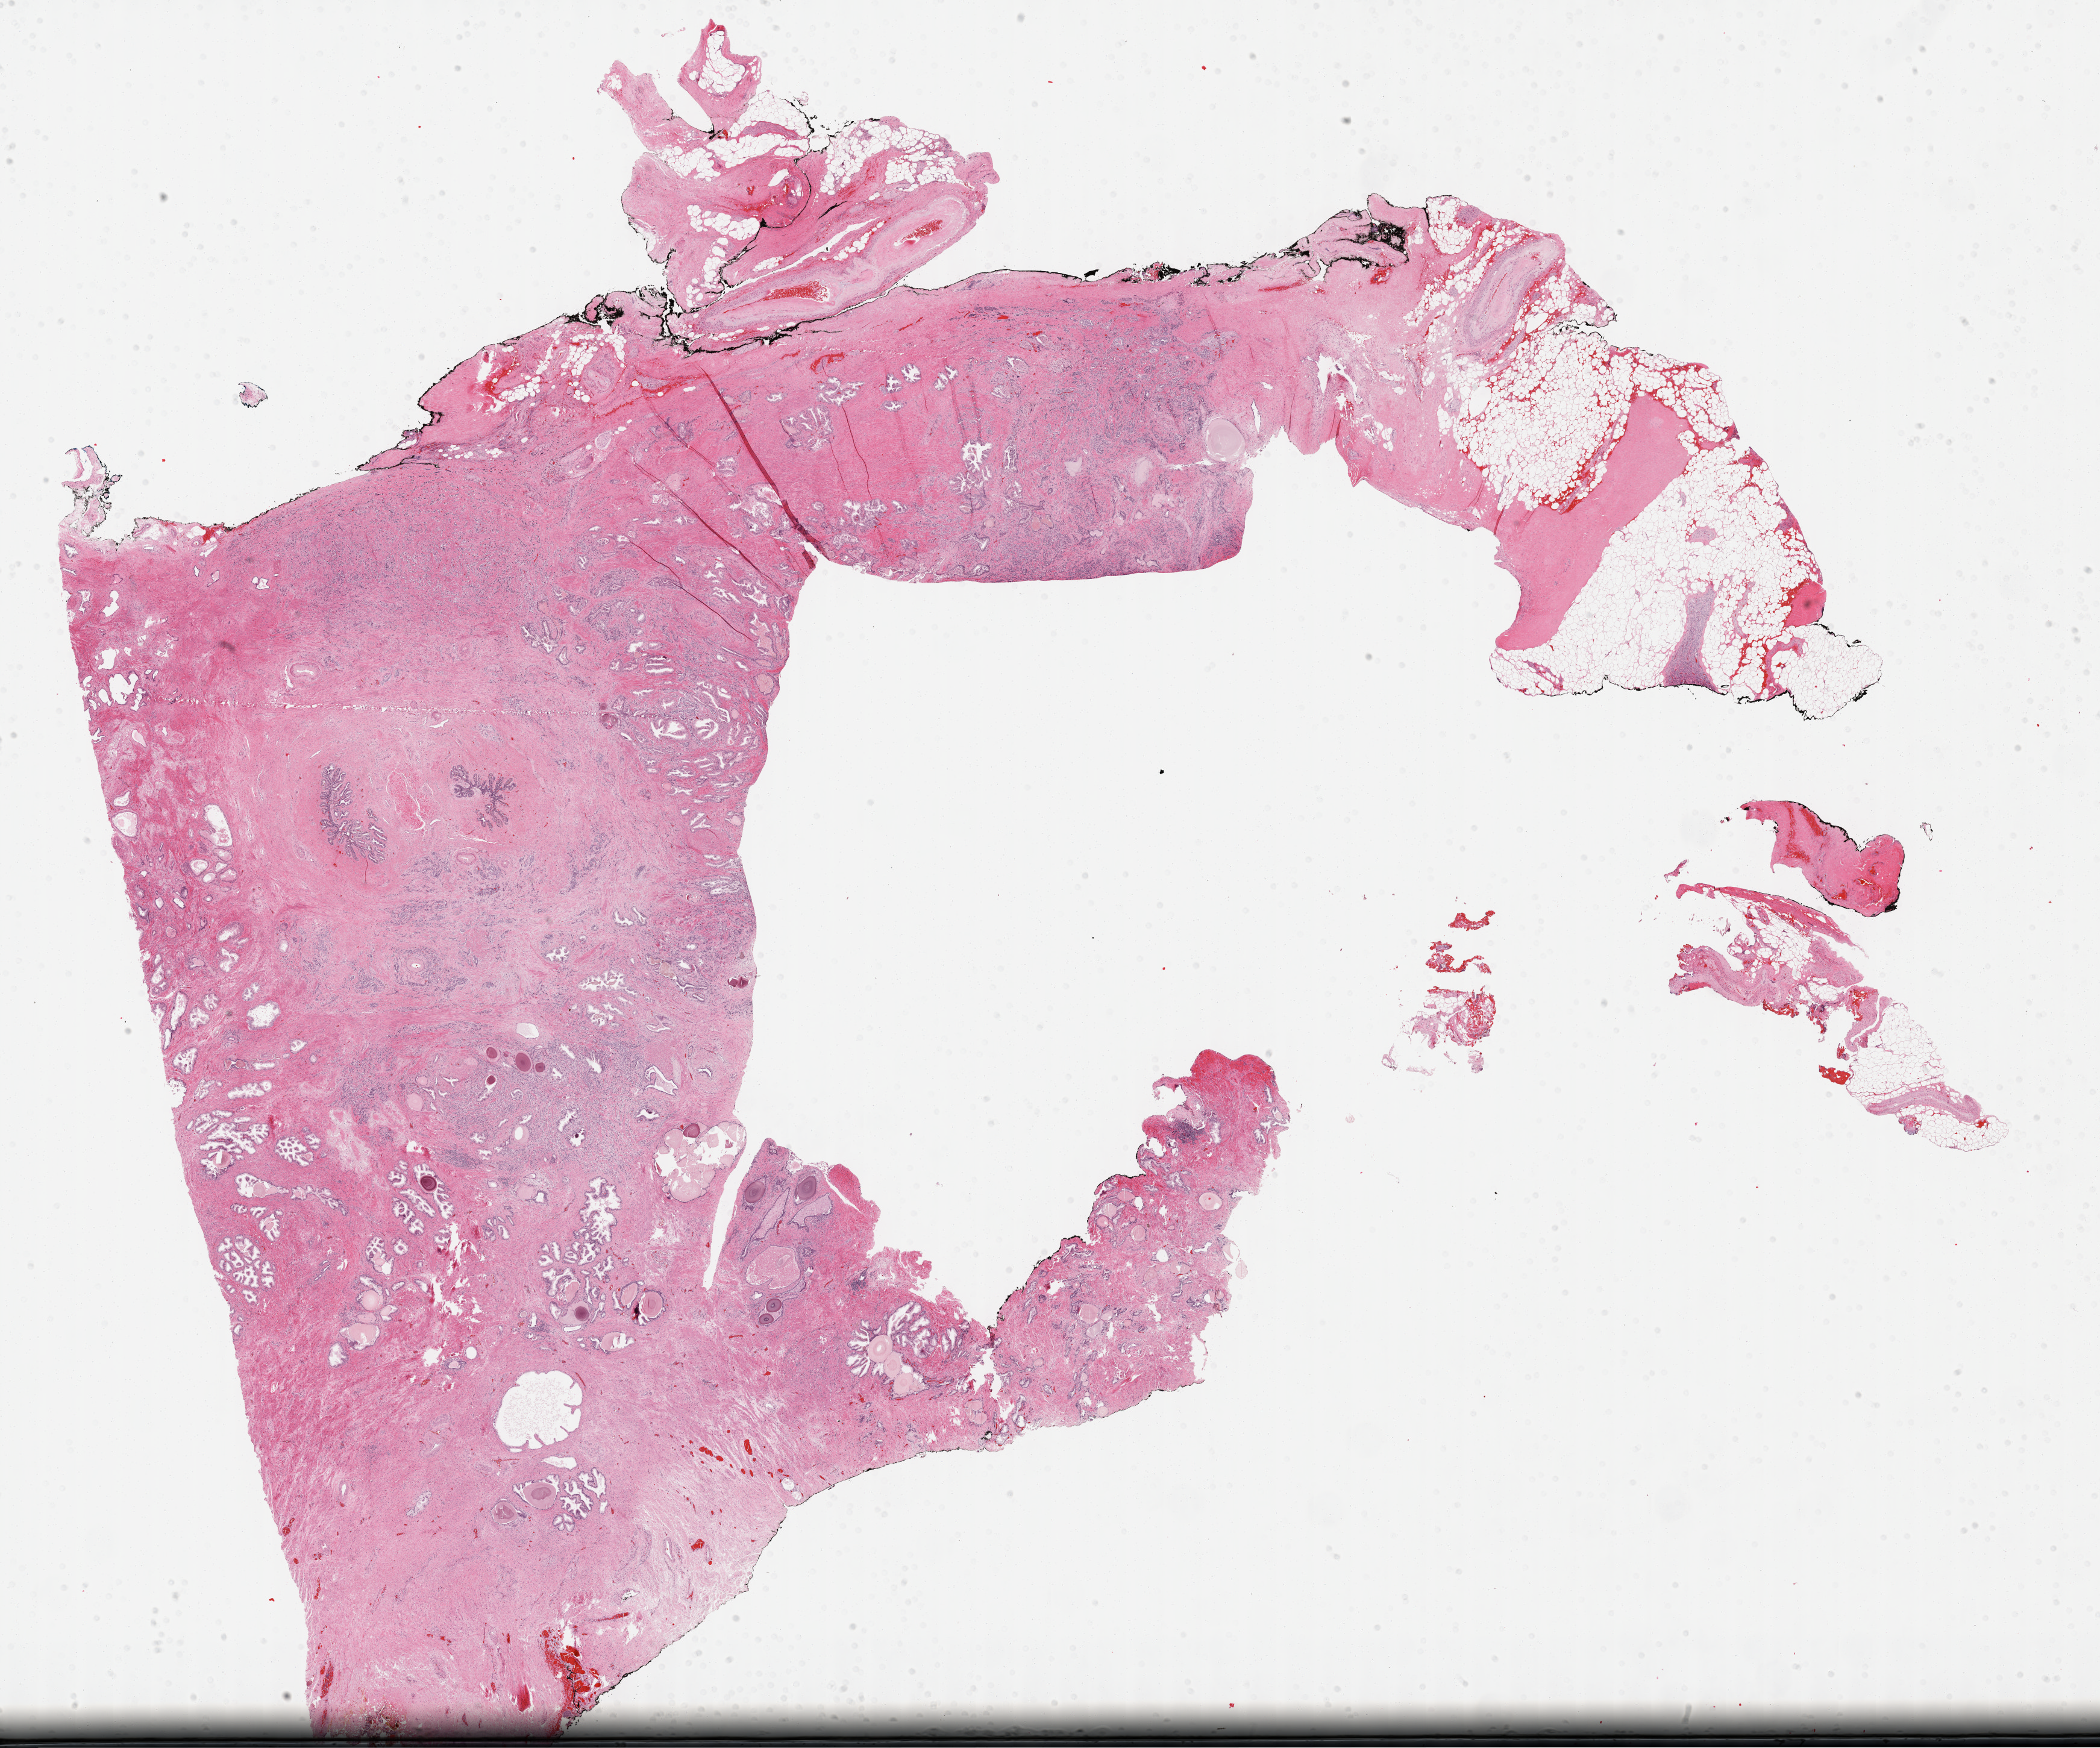
Whole-slide histology image, H&E — shown as a low-resolution overview of the whole scanned area (about 28.2 x 23.5 mm); FFPE section; sample: primary tumour, prostate. Male patient; age at initial diagnosis 65 years. Gleason score: 9 (4+5).
Diagnosis: Adenocarcinoma, NOS (prostate gland).